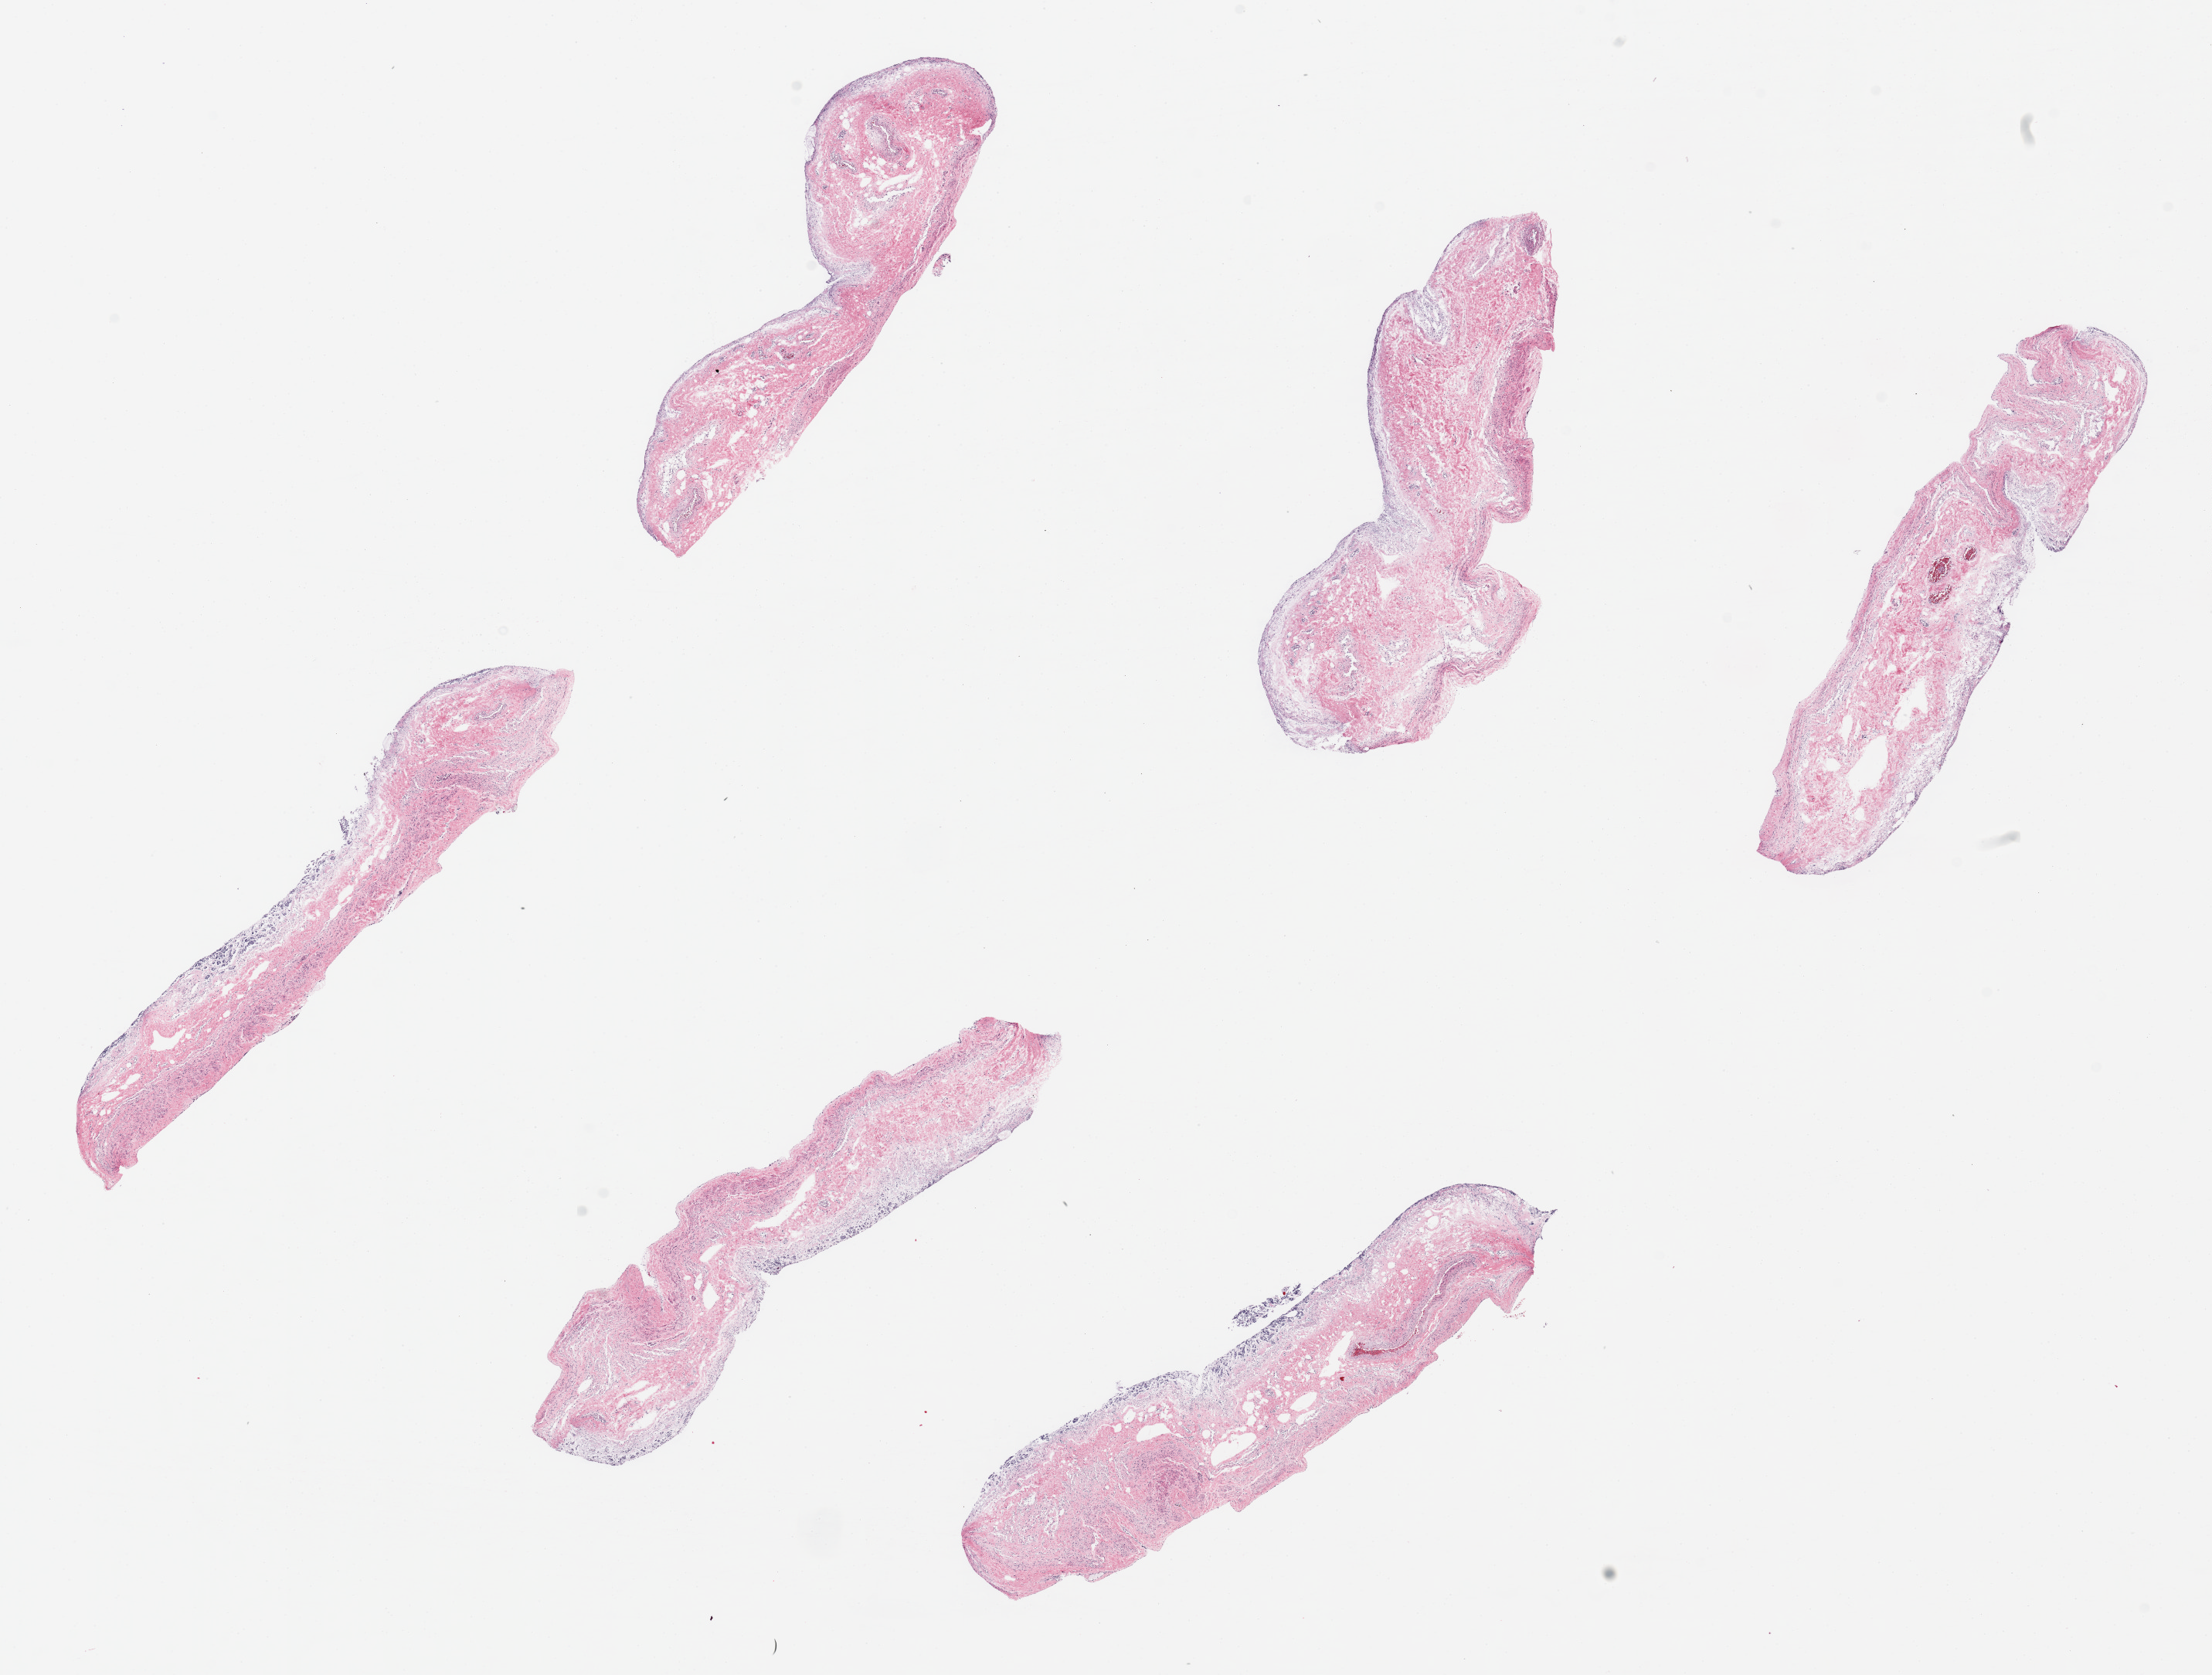
Digitized H&E-stained section — a low-resolution overview of the entire scanned area, about 22.6 x 17.1 mm (from a 20x scan), PAXgene-fixed paraffin-embedded (PFPE) section, target tissue: stomach, tissue donor sample. Donor sex: female.
Reviewer comment on this tissue sample: 6 pieces, up to 7x1mm; totally autolyzed mucosa; muscle also autolyzed; of limited molecular value.